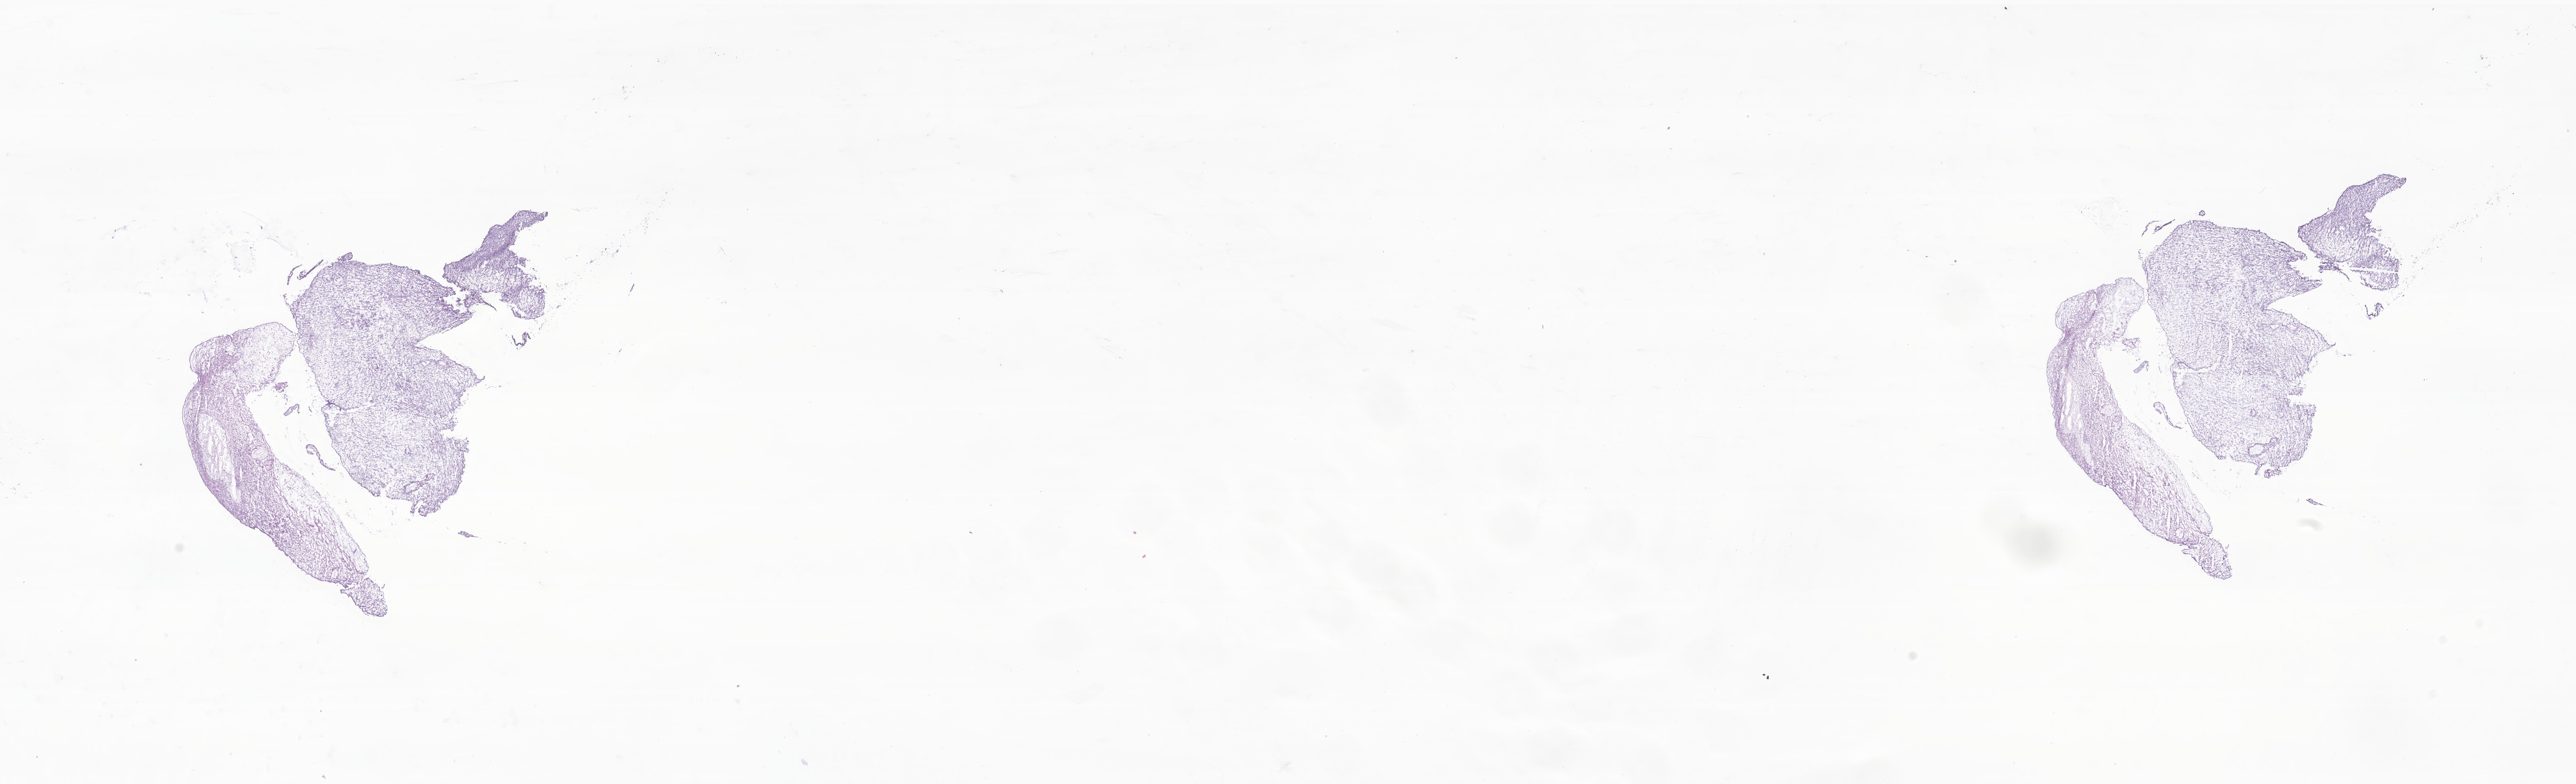
Digitized haematoxylin and eosin-stained section of tumor tissue from the bone, shown as a low-resolution overview of the whole scanned area (about 27.8 x 8.5 mm); frozen section (OCT-embedded). Patient female; age 41 months (3 years 5 months).
Recorded diagnosis: Rhabdomyosarcoma, NOS.